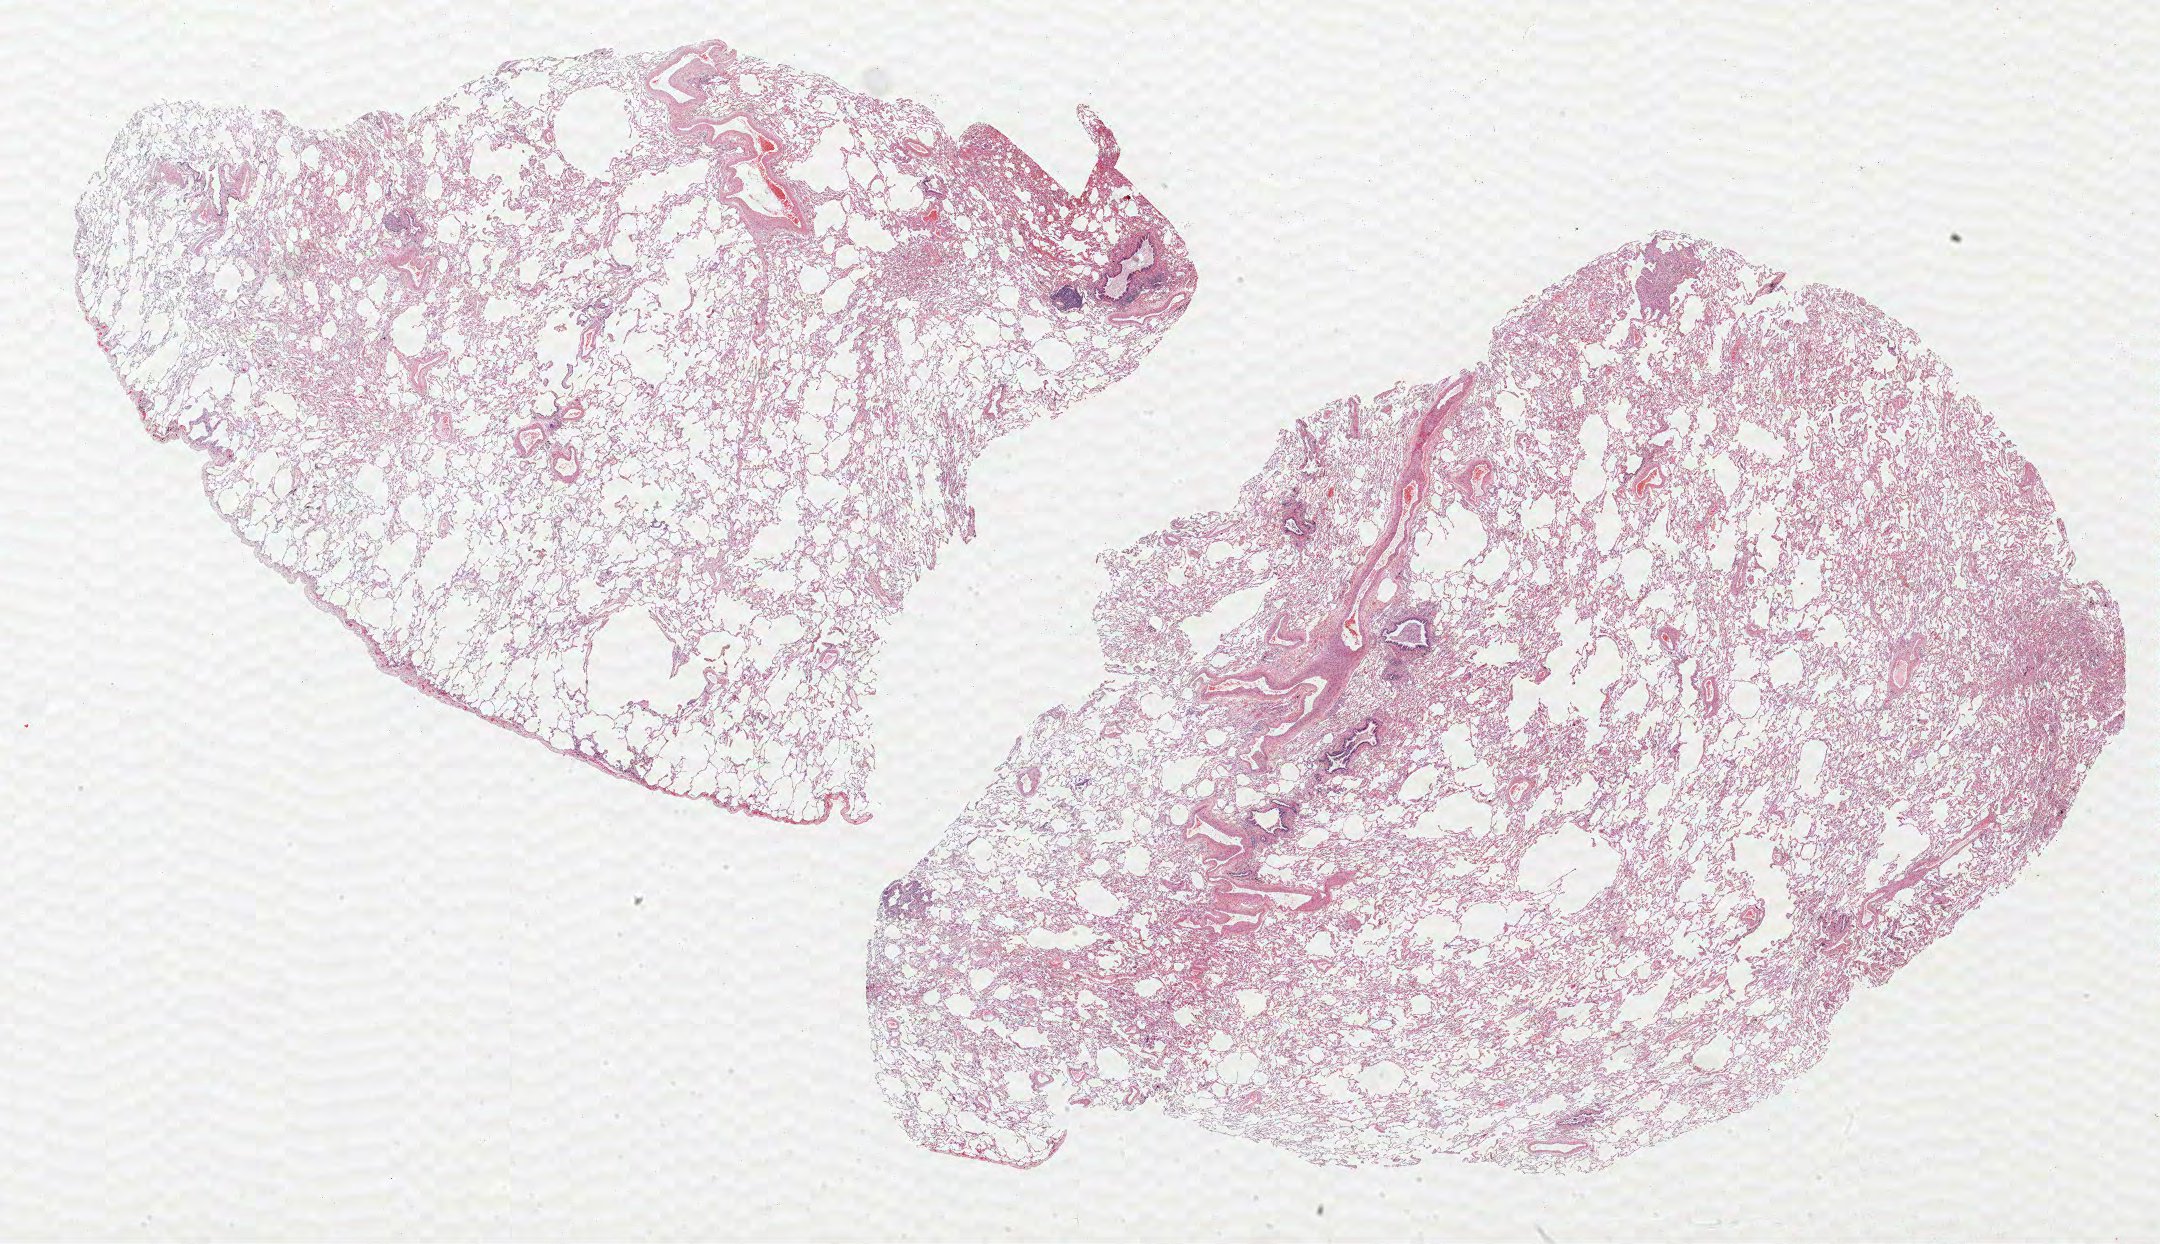
Whole-slide histology image, Hematoxylin and eosin (H&E) stained — low-resolution overview of the scanned area, about 34.6 x 19.9 mm (slide scanned at 40x), formalin-fixed paraffin-embedded (FFPE) section, lung. Female patient, aged 58 at enrolment. Former smoker at enrolment. Grade: moderately differentiated (G2).
• tumour size (pathology): 22 mm
• primary tumour location (clinical record): left upper lobe
• stage (AJCC 6th edition): IA
• participant's lung-cancer diagnosis: Squamous cell carcinoma, NOS